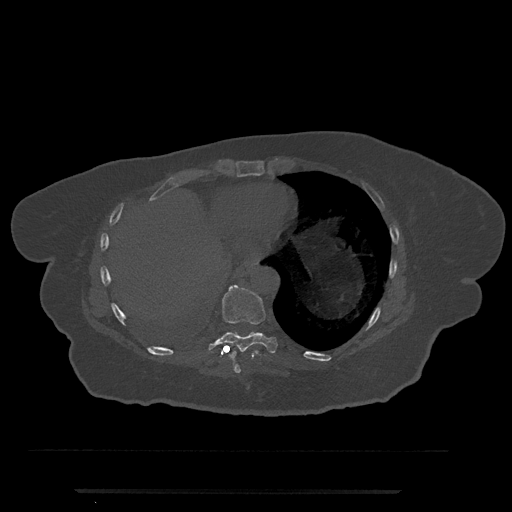
CT including the spine, one axial slice. Slice 336 of 797 in the series (ordered by position). Reconstruction kernel Br40s/3. 120 kVp. Bone window (W 1800 / L 400 HU). 0.5 mm slice thickness. 512 × 512 image matrix, field of view 440 × 440 mm. Patient: female, 51 years. From the clinical record (not read from this slice): primary cancer: neuro; vertebrae with lytic lesions (as recorded): T8.
Annotated regions visible in this slice (semi-automatically segmented with operator editing):
- T8 vertebra: bounding box (x1, y1, x2, y2) in pixels: (233, 354, 241, 373)
- T9 vertebra: (208, 285, 278, 358)